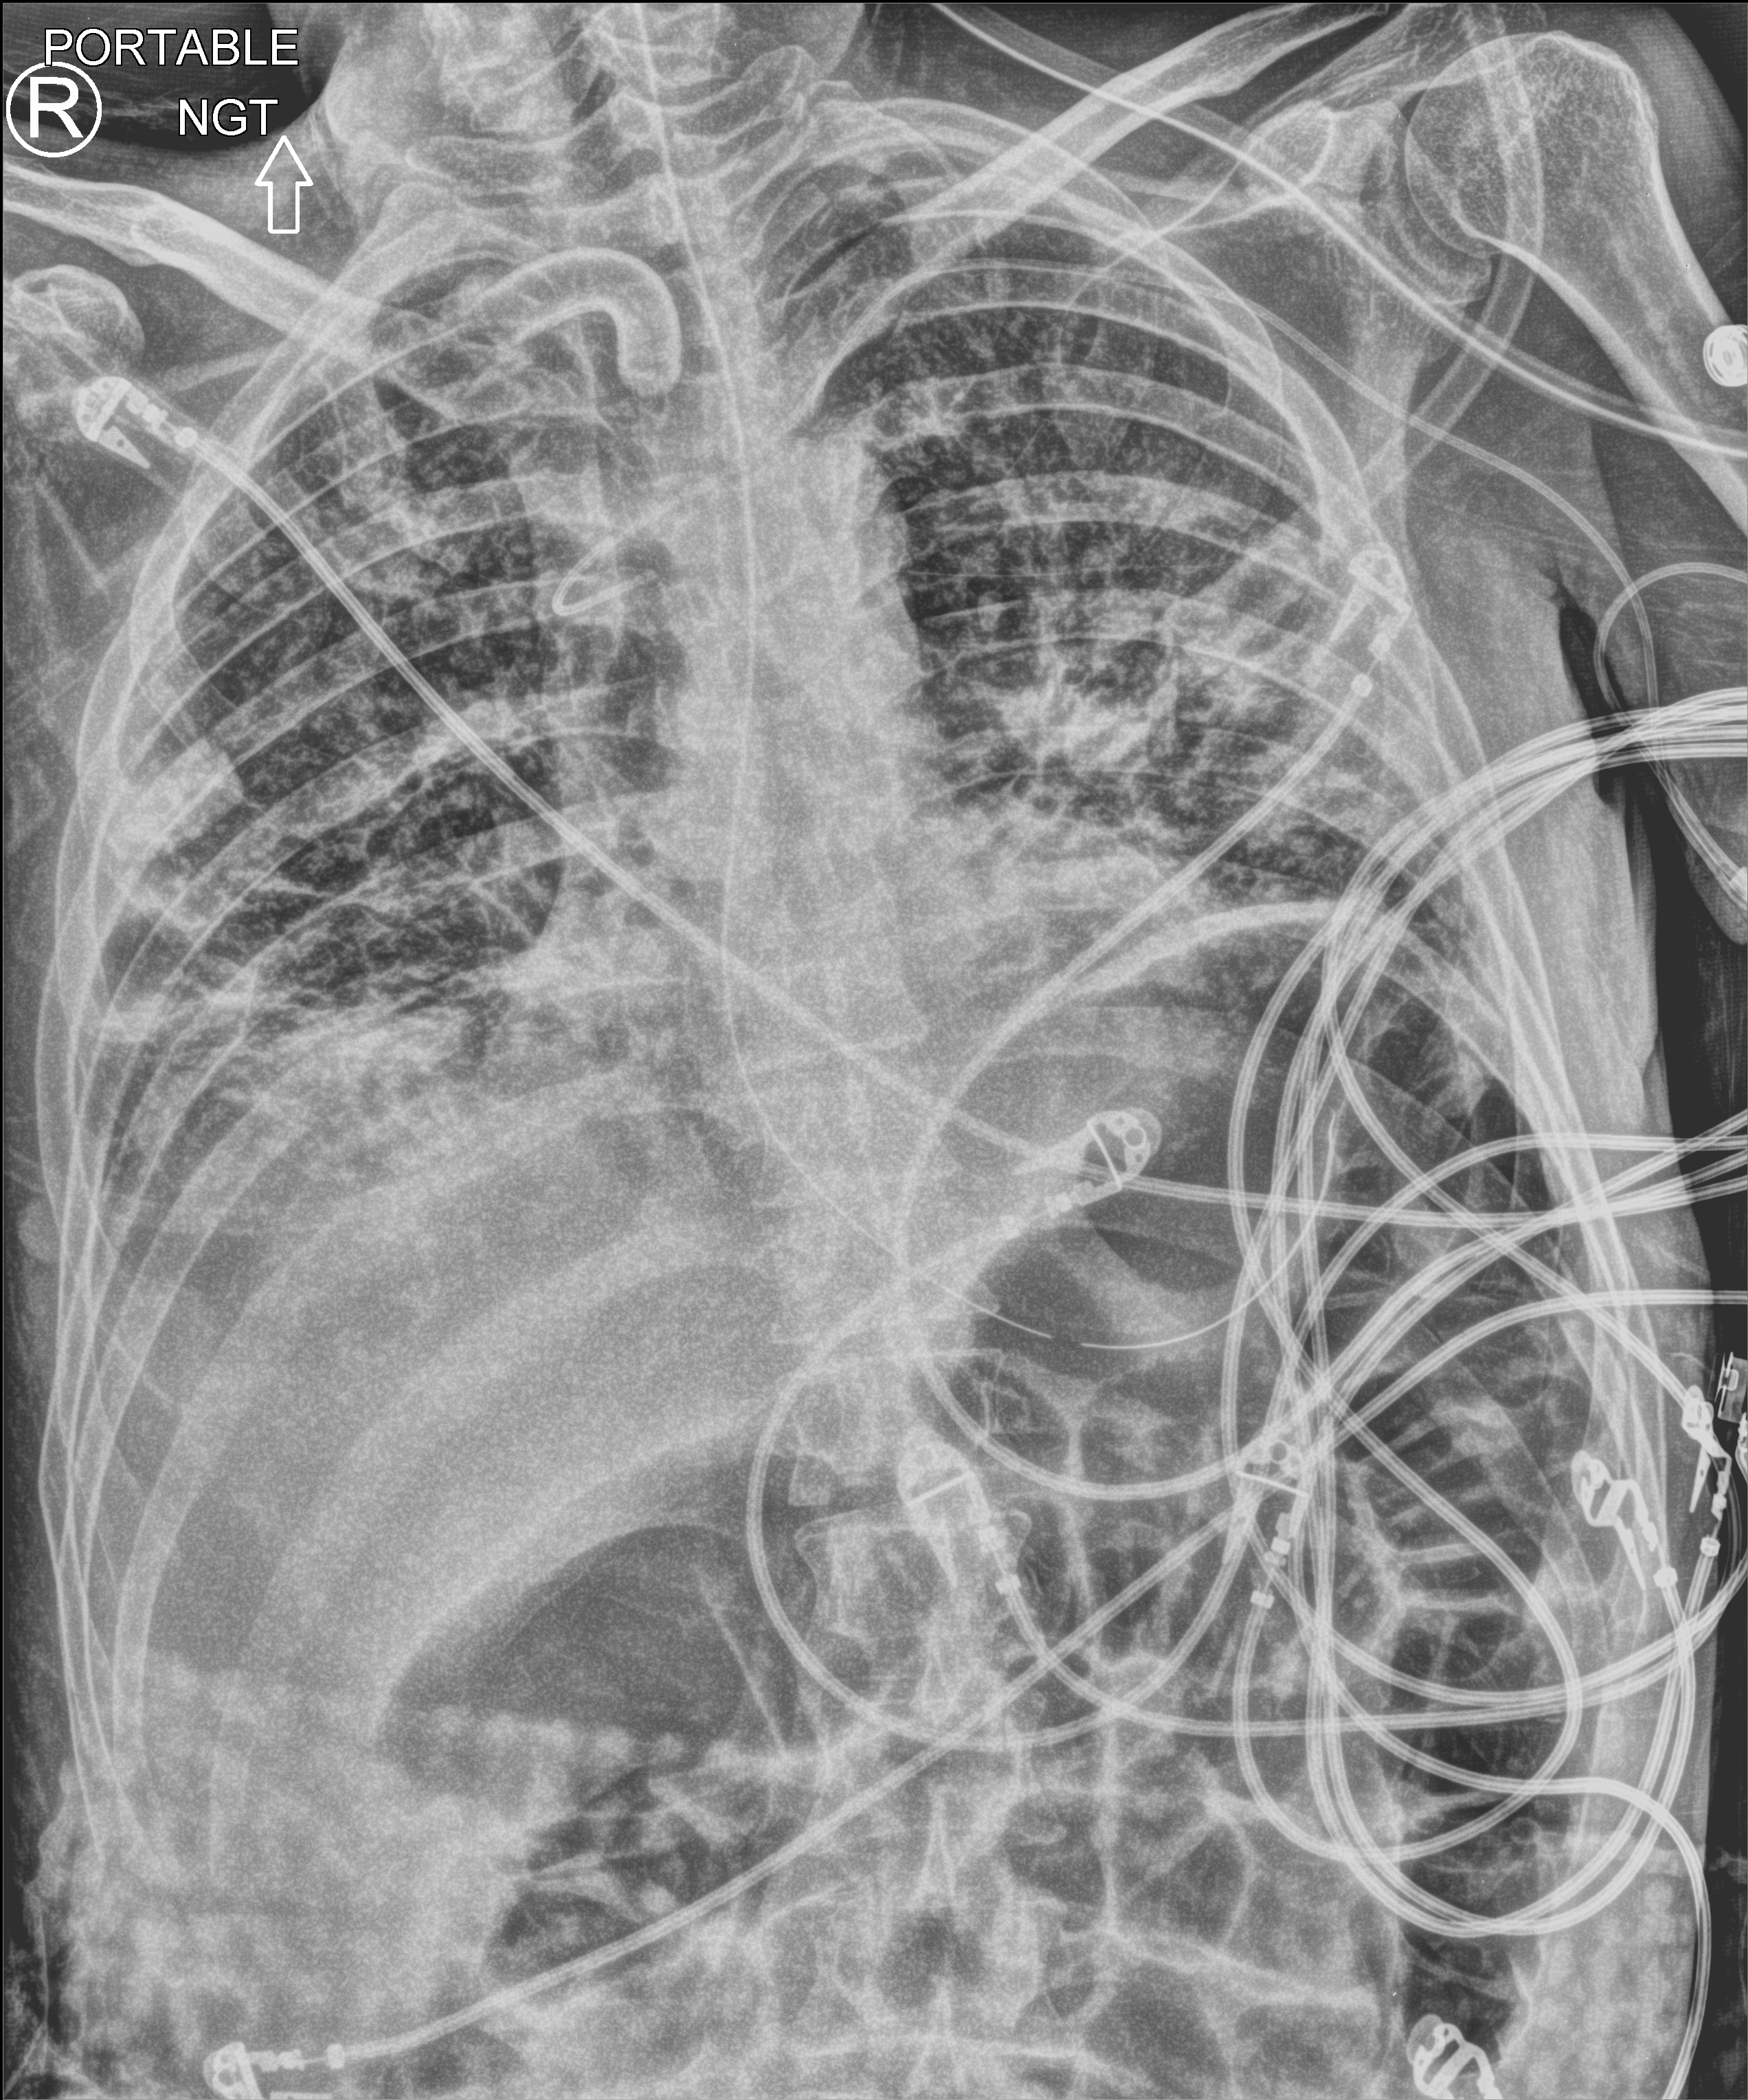
Bedside chest radiograph (computed radiography); anteroposterior (AP) projection. Male patient hospitalised with COVID-19, age 18–59 years.
Admission-level facts for this patient (not findings on this image; timing relative to this image not recorded):
- mechanically ventilated during this hospital stay: yes